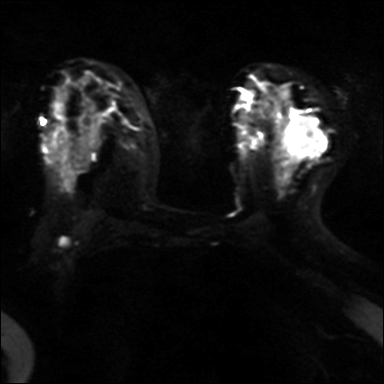
Breast MRI, one axial slice. Slice 22 of 40 in the series (ordered by position). Diffusion-weighted series; image 2 of 4 stored at this slice position (different b-values; order by instance number). 3 T. 384 × 384 image matrix, field of view 320 × 320 mm. Female patient.
Structures marked on this image (outlined manually by an expert reader):
- tumour on diffusion-weighted imaging: bounding box <293,116,324,157> (left, top, right, bottom; pixels)